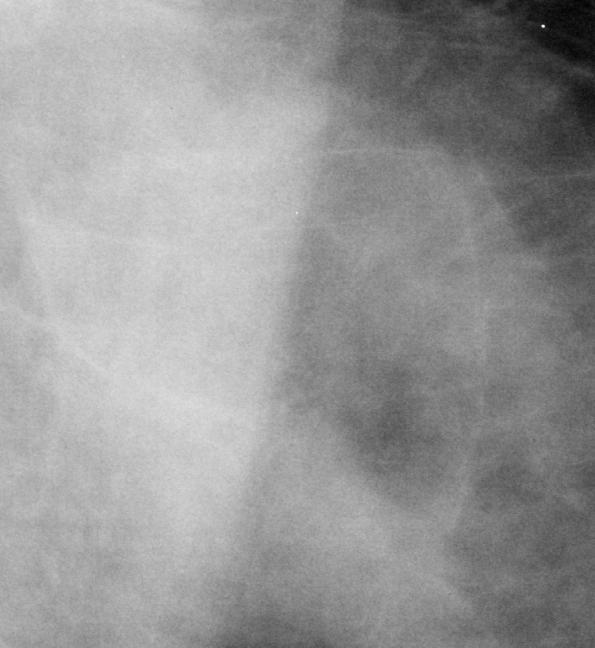
Region of interest cut from a scanned film mammogram (one marked finding); left breast; MLO view.
Mass, shape focal asymmetric density; BI-RADS assessment category 2; subtlety rating 4 on a 1 (subtle) to 5 (obvious) scale; benign; no additional work-up was recommended (benign without callback).